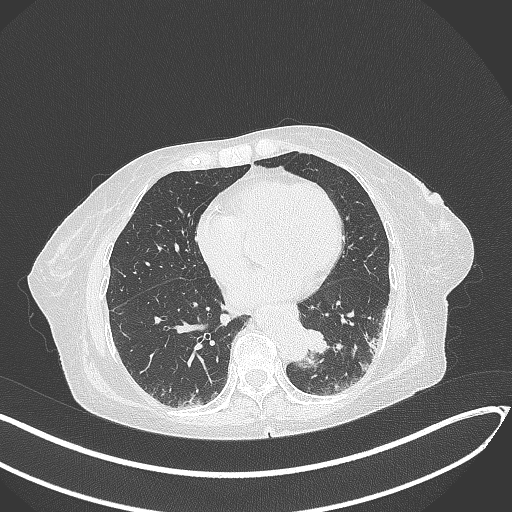
Chest CT, one axial slice; slice 83 of 324 in the series (ordered by position); lung window (W 1500 / L -600 HU); 512 × 512 image matrix, field of view 400 × 400 mm. Patient: female, 82 years. From the clinical record (not read from this slice): clinical TNM (as recorded): T1b N0 M1.
Annotated regions visible in this slice (bounding box drawn by a radiologist):
- lung tumour (recorded histology: adenocarcinoma): box from (x=300, y=324) to (x=337, y=362) px